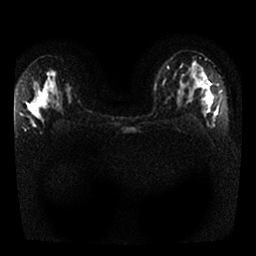
Breast MRI, one axial slice. Position 16 of 25 along the scan axis. Diffusion-weighted series; image 2 of 4 stored at this slice position (different b-values; order by instance number). 1.5 T. 256 × 256 image matrix. Female patient.
Annotated regions visible in this slice (outlined manually by an expert reader):
- tumour on diffusion-weighted imaging: box from (x=197, y=64) to (x=209, y=85) px